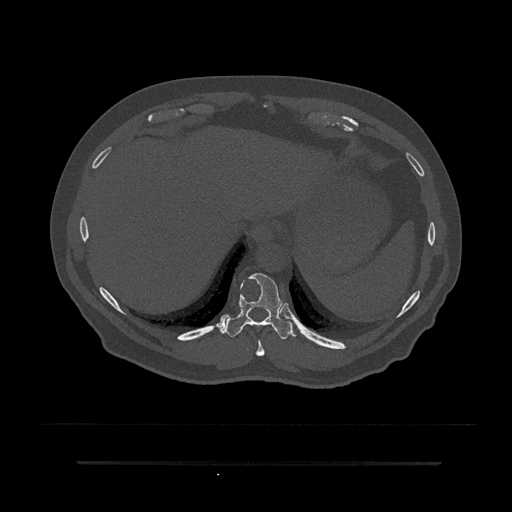
CT including the spine, one axial slice. Position 335 of 797 along the scan axis. Bone window (W 1800 / L 400 HU). 0.5 mm slice thickness. 512 × 512 image matrix, field of view 464 × 464 mm. Patient: male, 59 years. From the clinical record (not read from this slice): primary cancer: bile ducts; vertebrae with lytic lesions (as recorded): T10.
Outlined on this slice (semi-automatically segmented with operator editing):
- T10 vertebra: bounding box <223,273,296,339> (left, top, right, bottom; pixels)
- T9 vertebra: <255,340,265,356>